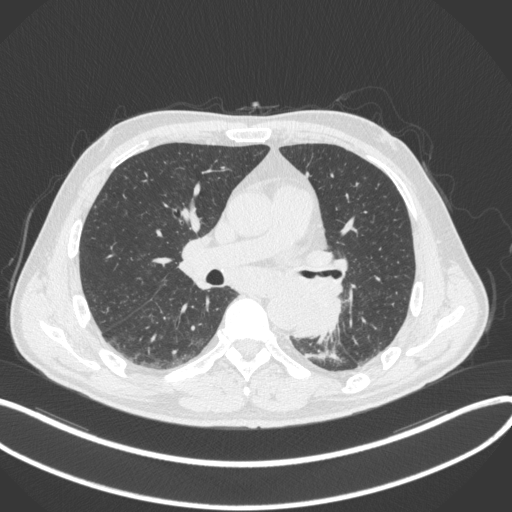
Chest CT, one axial slice. Position 185 of 328 along the scan axis. 120 kVp. Lung window (W 1500 / L -600 HU). 1 mm slice thickness. 512 × 512 image matrix, field of view 400 × 400 mm. Patient: male, 59 years. Case-level facts recorded for this patient, not image findings: clinical TNM (as recorded): T2a N2 M0.
Structures marked on this image (rectangle marked by the reading radiologist):
- lung tumour (recorded histology: squamous cell carcinoma): bounding box [x1, y1, x2, y2] px = [291, 290, 346, 341]